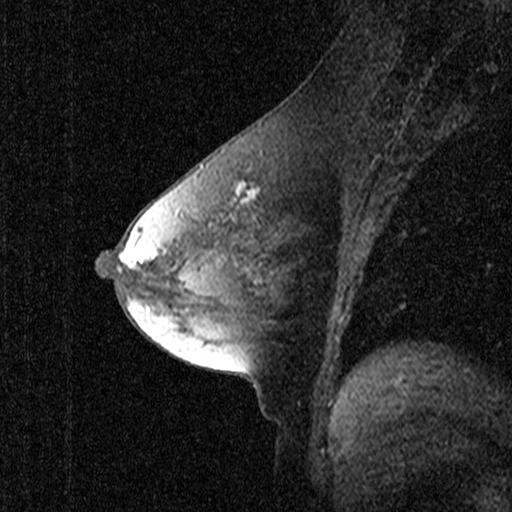
Breast MRI (dynamic contrast-enhanced), one sagittal slice; position 26 of 44 along the scan axis; dynamic contrast-enhanced study with each time point stored as its own series, time point 2 of 3 at this slice position (early post-contrast, ordered by acquisition time); 1.5 T; TE 4.5 ms, TR 11 ms; 2.27 mm slice thickness; 512 × 512 image matrix, field of view 200 × 200 mm. Female patient, age 53 years. Case-level facts recorded for this patient, not image findings: setting: breast cancer imaged before/during neoadjuvant chemotherapy; receptor status: HR-positive, HER2-negative.
Annotated regions visible in this slice (semi-automatically segmented with operator editing):
- analysis volume of interest (the breast-tissue region the enhancement analysis was run in; not a lesion): box from (x=192, y=146) to (x=303, y=281) px
- tumour enhancement mask (voxels above the 90 % enhancement threshold inside the analysis volume of interest): (x=239, y=183)–(x=257, y=198)